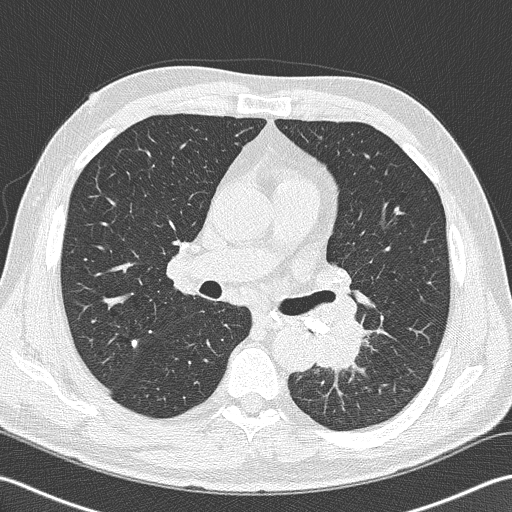
Low-dose screening chest CT, axial slice. Second annual screen. Lung window (W 1500 / L -600 HU). Lung (sharp) reconstruction kernel (B50f). Slice 70 of 170 in the series. 512 × 512 image matrix. Male participant, aged 57 years at enrolment.
Expert-annotated lung lesion, bounding box <294,305,374,383> (left, top, right, bottom; pixels). The exam's reader record, not a measurement of the box and not confirmed to be the same lesion: non-calcified nodule or mass ≥4 mm, left lower lobe, 40 × 30 mm, spiculated (stellate) margins, soft tissue attenuation, pre-existing on the prior screen: no. Later outcome: lung cancer diagnosed 9 days after this screen — squamous cell carcinoma, NOS, left lower lobe, moderately differentiated (G2), stage IIIB (AJCC 6th edition), 38 mm at pathology.